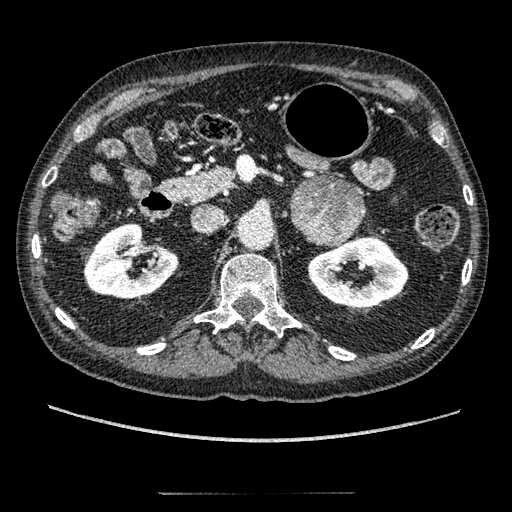
Contrast-enhanced abdominal CT, one axial slice; position 114 of 274 along the scan axis; 120 kVp; intravenous contrast given; soft-tissue window (W 400 / L 40 HU); 512 × 512 image matrix, field of view 381 × 381 mm. Male patient, age 69 years. From the clinical record (not read from this slice): diagnosis: adrenocortical carcinoma; tumour side: left adrenal; tumour size at pathology: 6.1 cm; Ki-67 index: 10 %; stage (as recorded): 3.
Annotated regions visible in this slice (semi-automatically segmented with operator editing):
- mass: bounding box <292,176,364,245> (left, top, right, bottom; pixels)